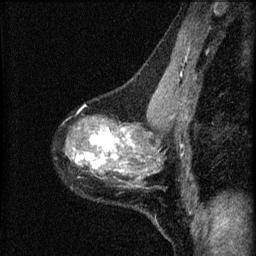
Breast MRI (dynamic contrast-enhanced), one sagittal slice. Position 38 of 60 along the scan axis. Dynamic contrast-enhanced series, image 2 of 4 at this slice position (ordered by acquisition). 1.5 T. TE 4.2 ms, TR 8.2 ms. 2 mm slice thickness. 256 × 256 image matrix, field of view 180 × 180 mm. Patient: female, 41 years.
Annotated regions visible in this slice (semi-automatic segmentation, software-assisted and operator-edited):
- analysis volume of interest (the breast-tissue region the enhancement analysis was run in; not a lesion): bounding box <64,91,166,189> (left, top, right, bottom; pixels)
- tumour enhancement mask (voxels above the 70 % enhancement threshold inside the analysis volume of interest): <73,127,135,173>